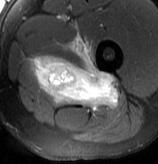
MRI of an extremity soft-tissue mass, one axial slice; position 56 of 70 along the scan axis; T2-weighted fat-saturated; MR volume resampled by the dataset authors to the PET/CT grid (not the native acquisition matrix); 158 × 164 image matrix, field of view 154 × 160 mm. Male patient. Case-level facts recorded for this patient, not image findings: histological type: extraskeletal osteosarcoma; grade: high; site of the primary tumour: left adductur.
Structures marked on this image (expert contour drawn on MRI and transferred to this co-registered scan by the dataset authors):
- gross tumour volume (mass): bounding box <29,35,119,111> (left, top, right, bottom; pixels)